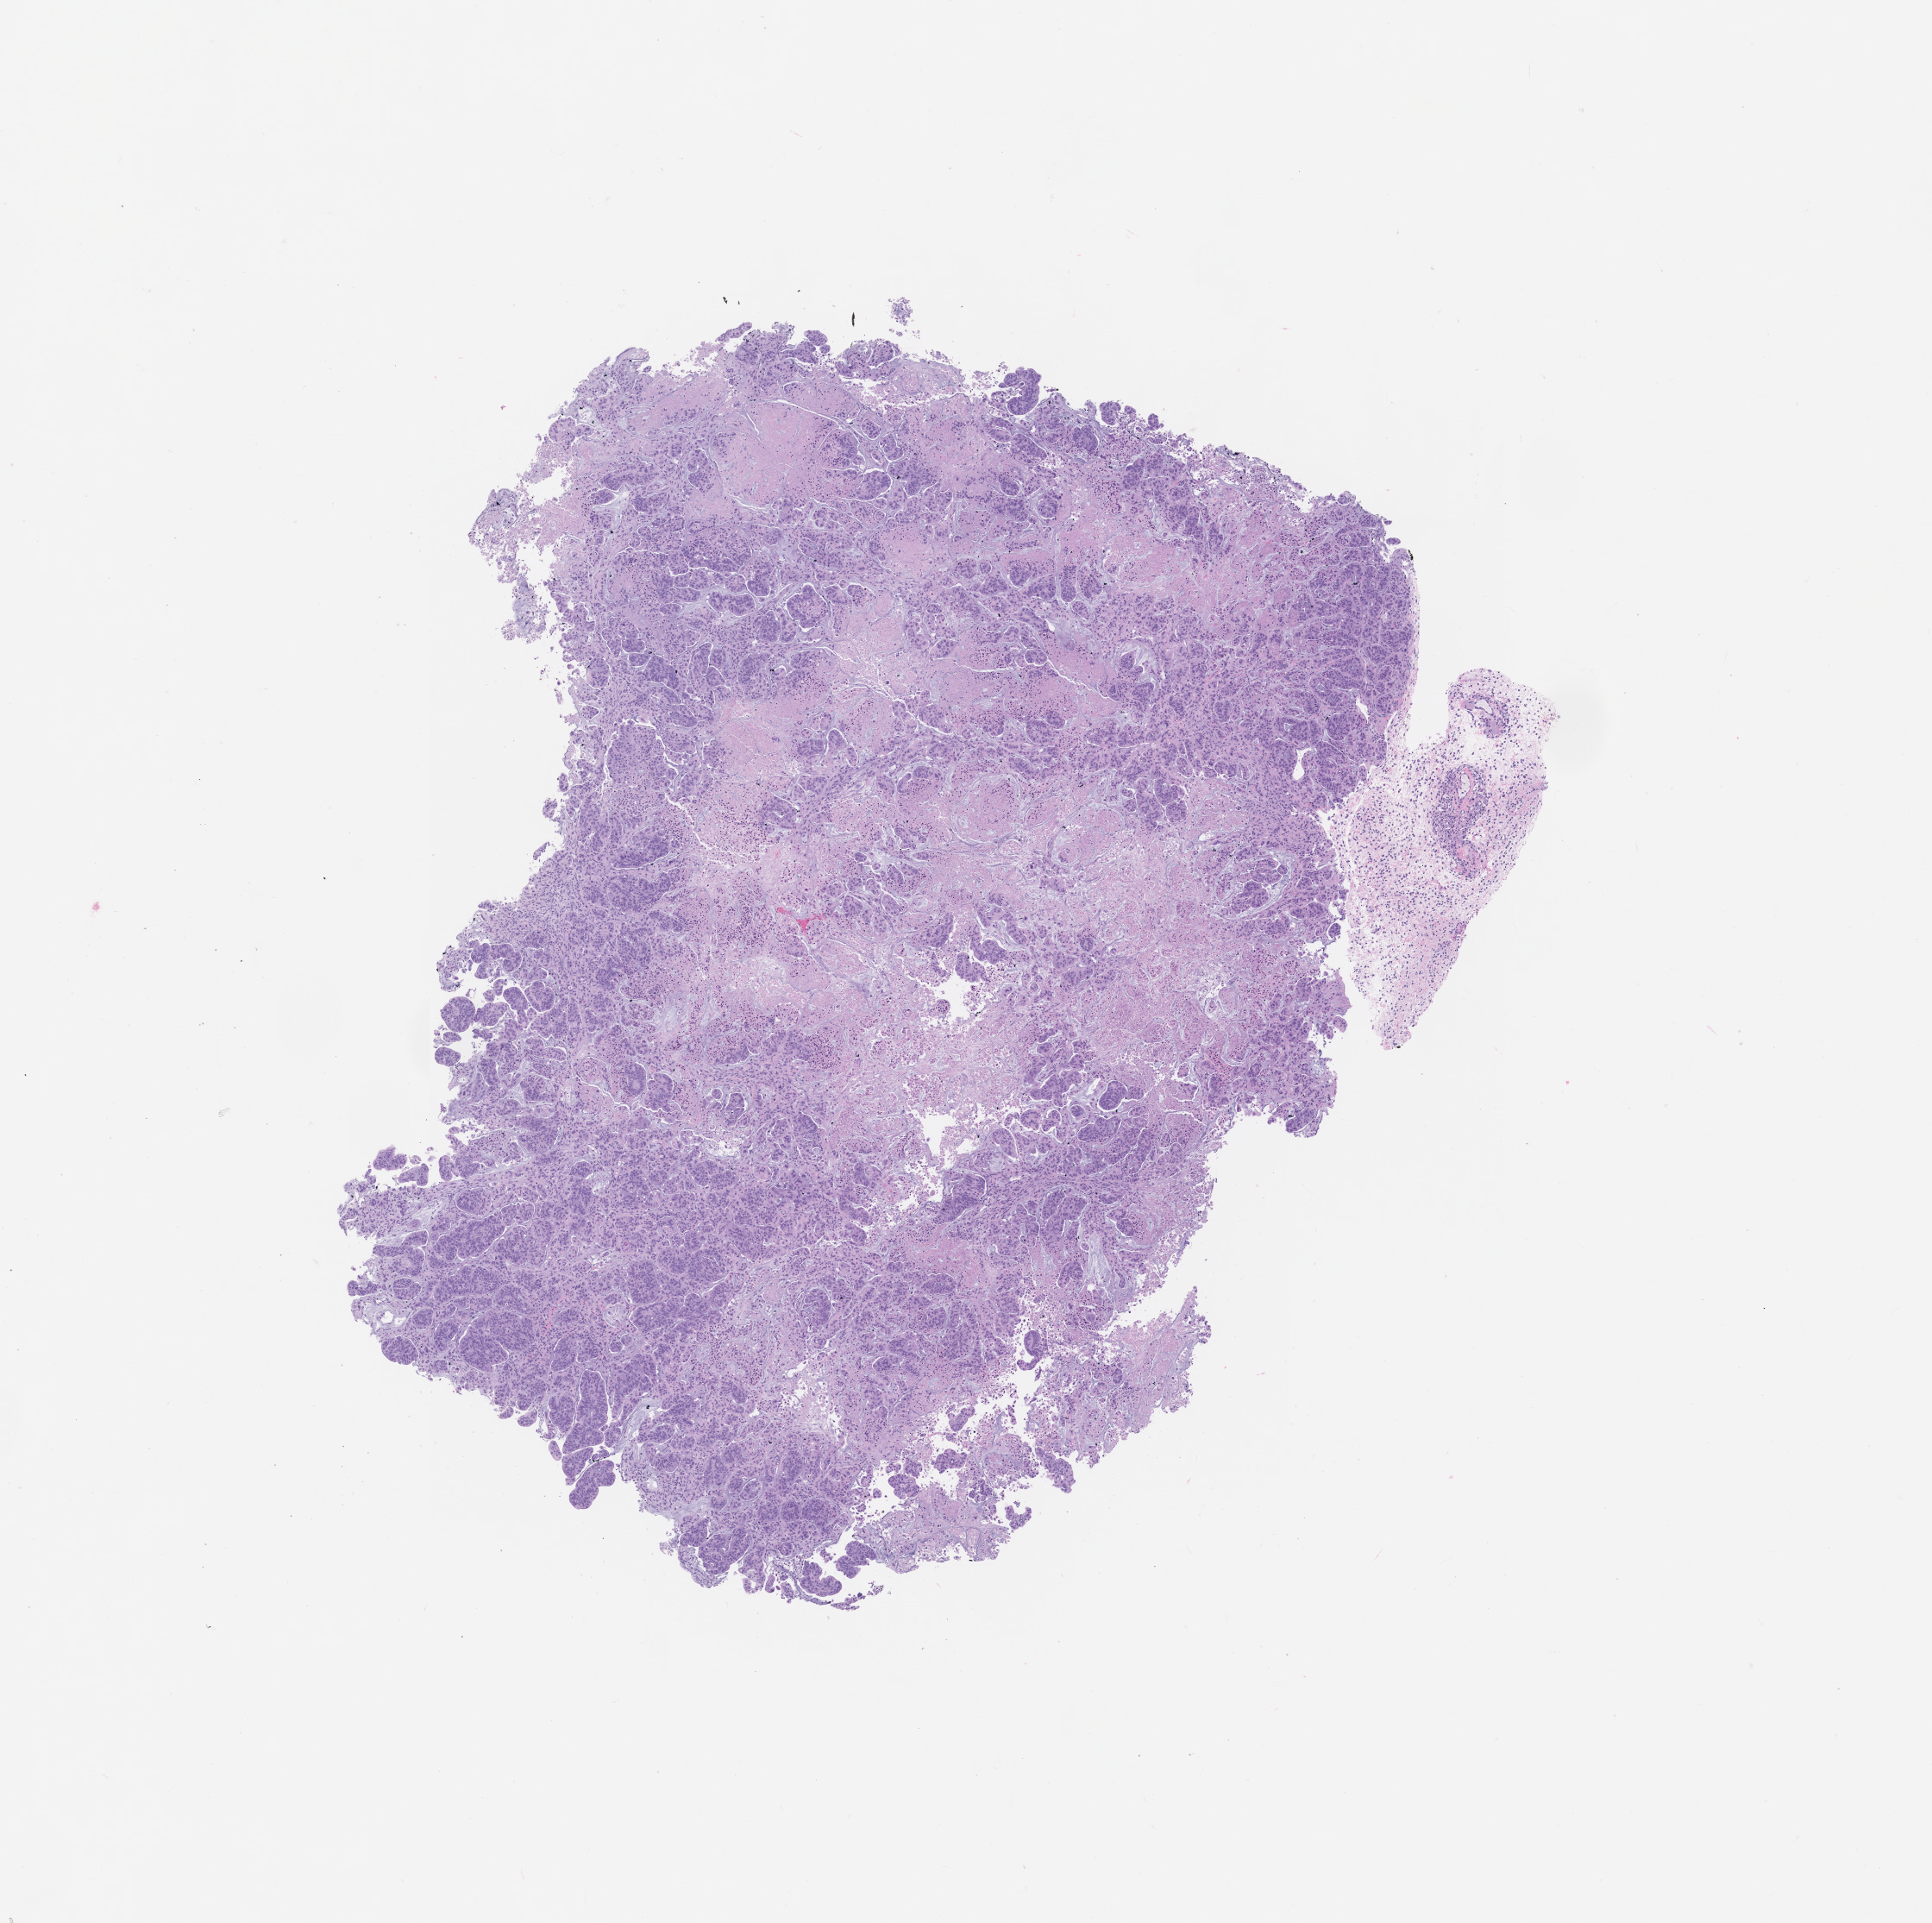
Whole-slide image, H&E: patient-derived xenograft (human tumor grown in a mouse), passage 2, low-resolution overview of the scanned area, about 9.0 x 8.9 mm. Formalin-fixed, paraffin-embedded (FFPE) tissue. Originating tumor site category: small intestine.
Originating patient diagnosis: Small Intestinal Adenocarcinoma.